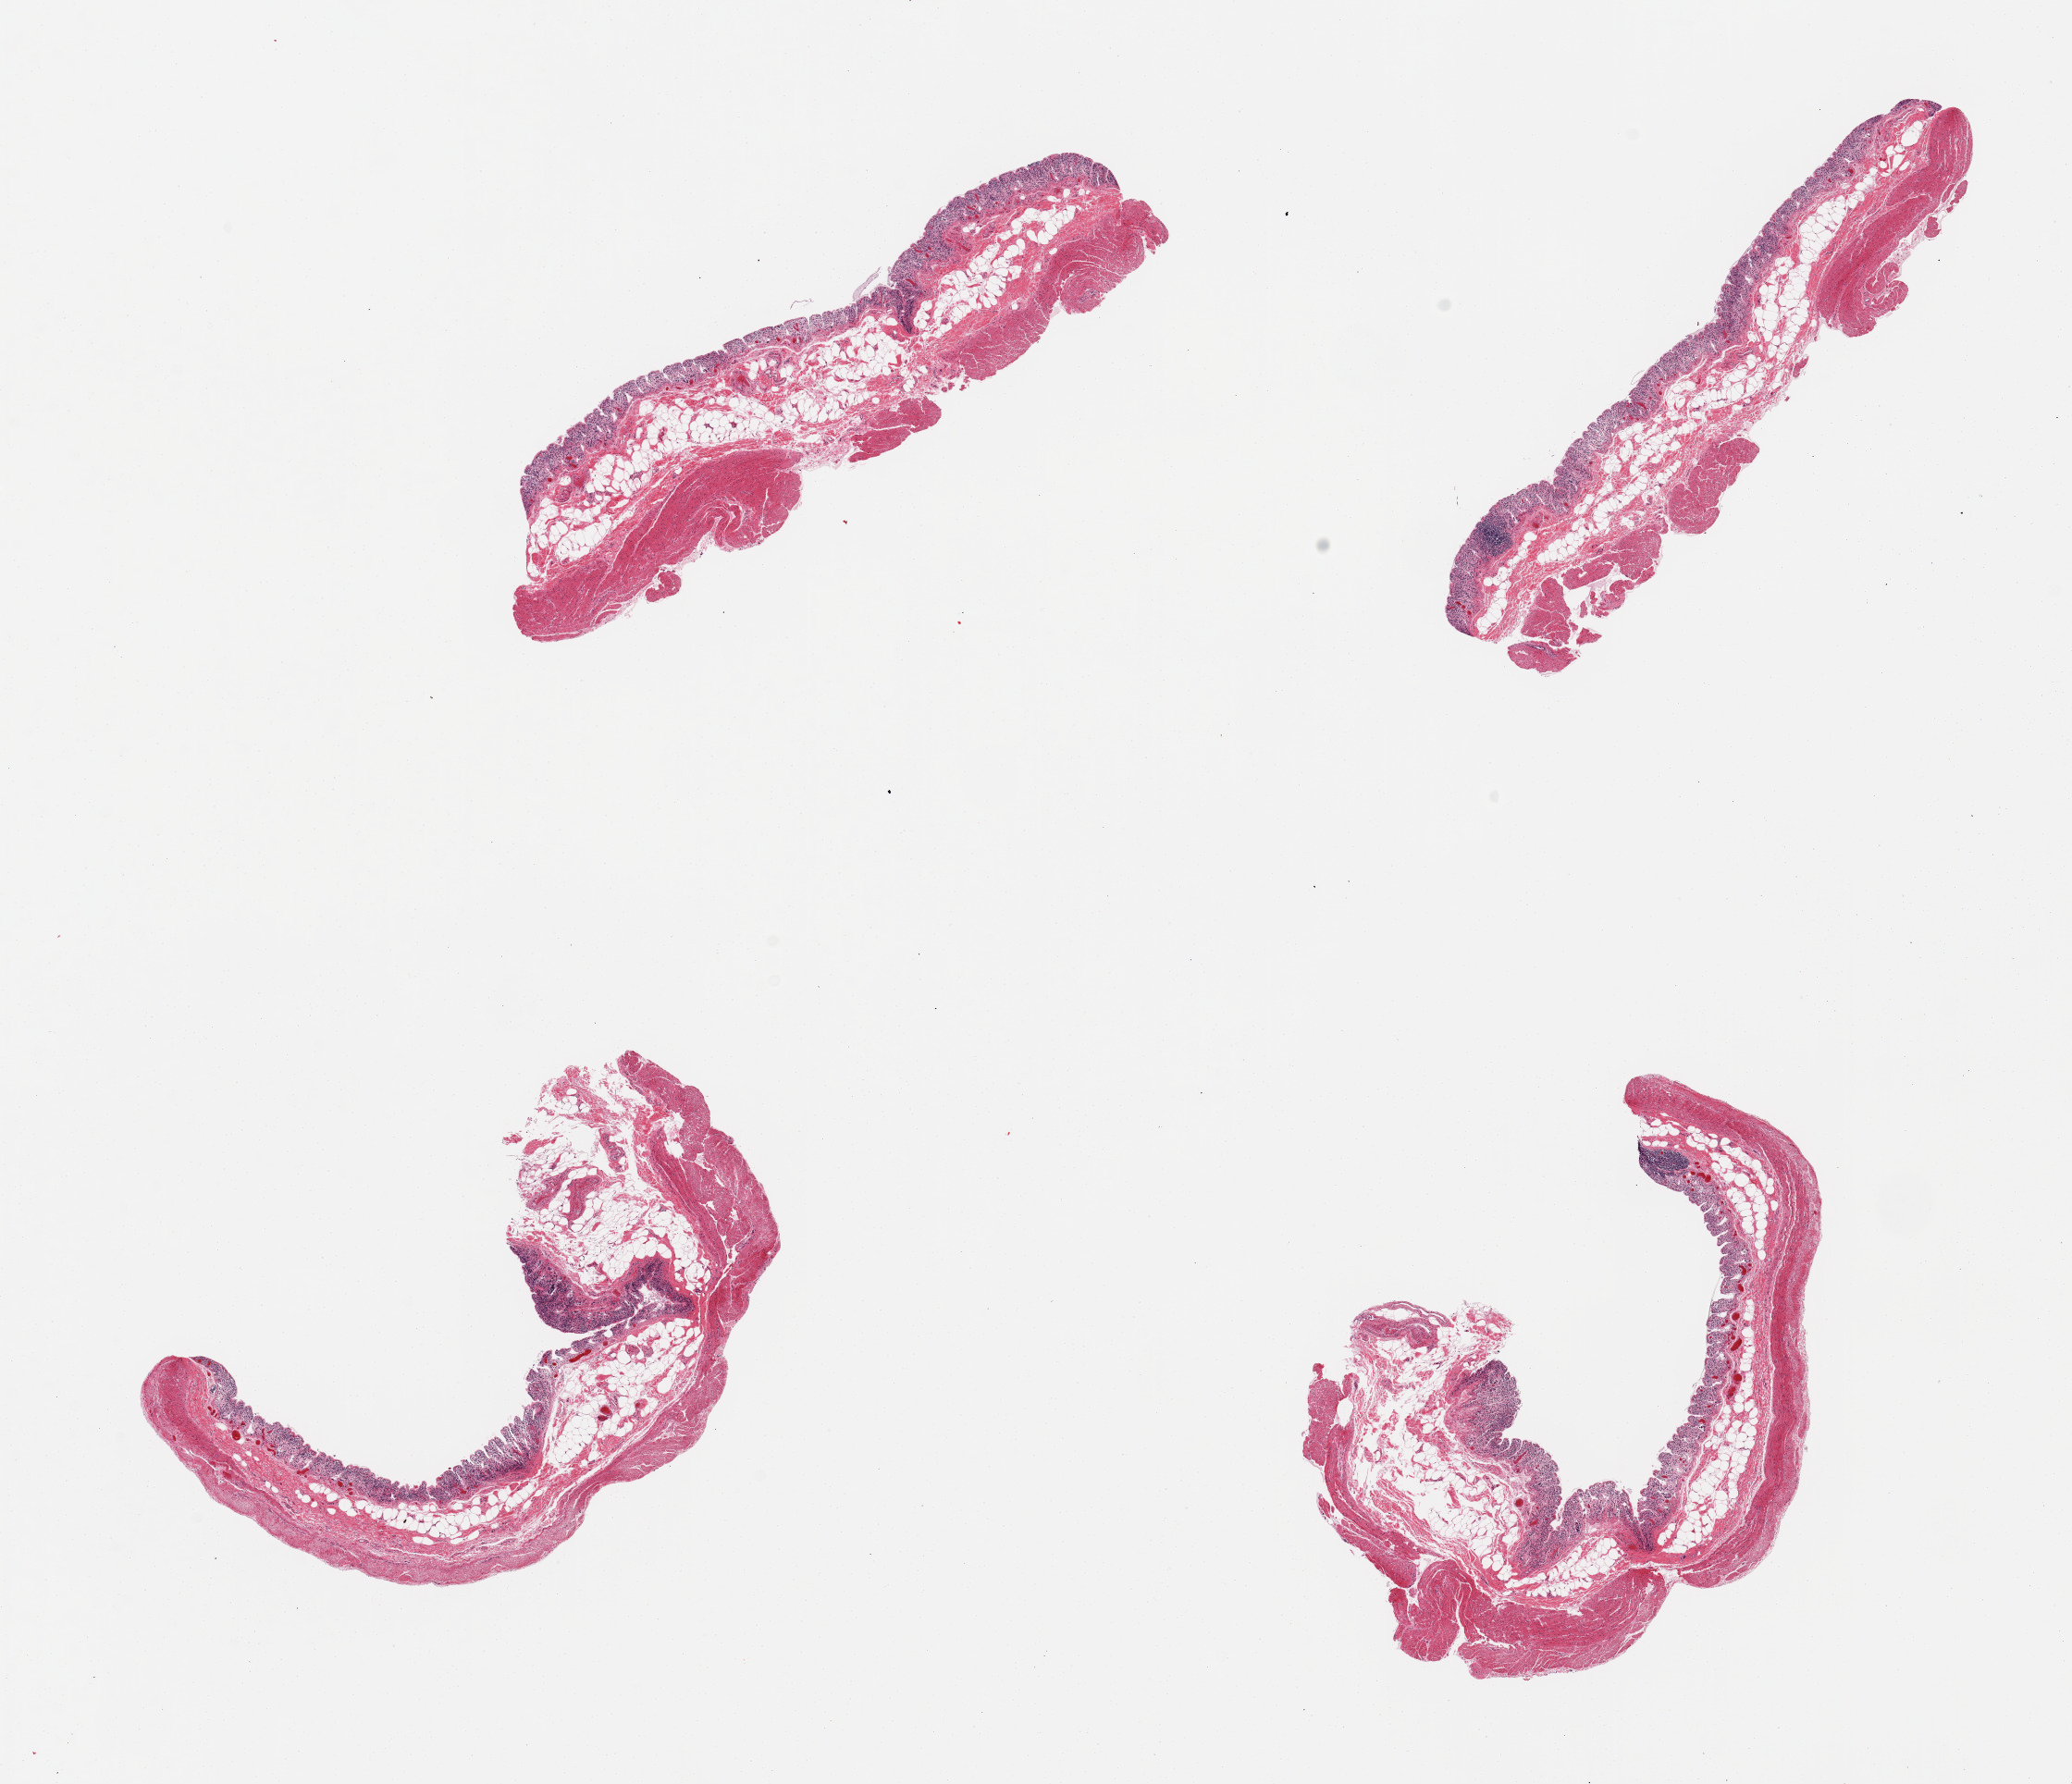
Haematoxylin and eosin whole-slide image, whole scanned area (about 17.7 x 15.3 mm) shown as a low-resolution overview. PAXgene-fixed paraffin-embedded (PFPE) section. Sampled site (target tissue): transverse colon. Donor tissue sample. Donor: female.
Reviewer comment on this tissue sample: 4 pieces; mucosa autolyzed; muscularis intact.